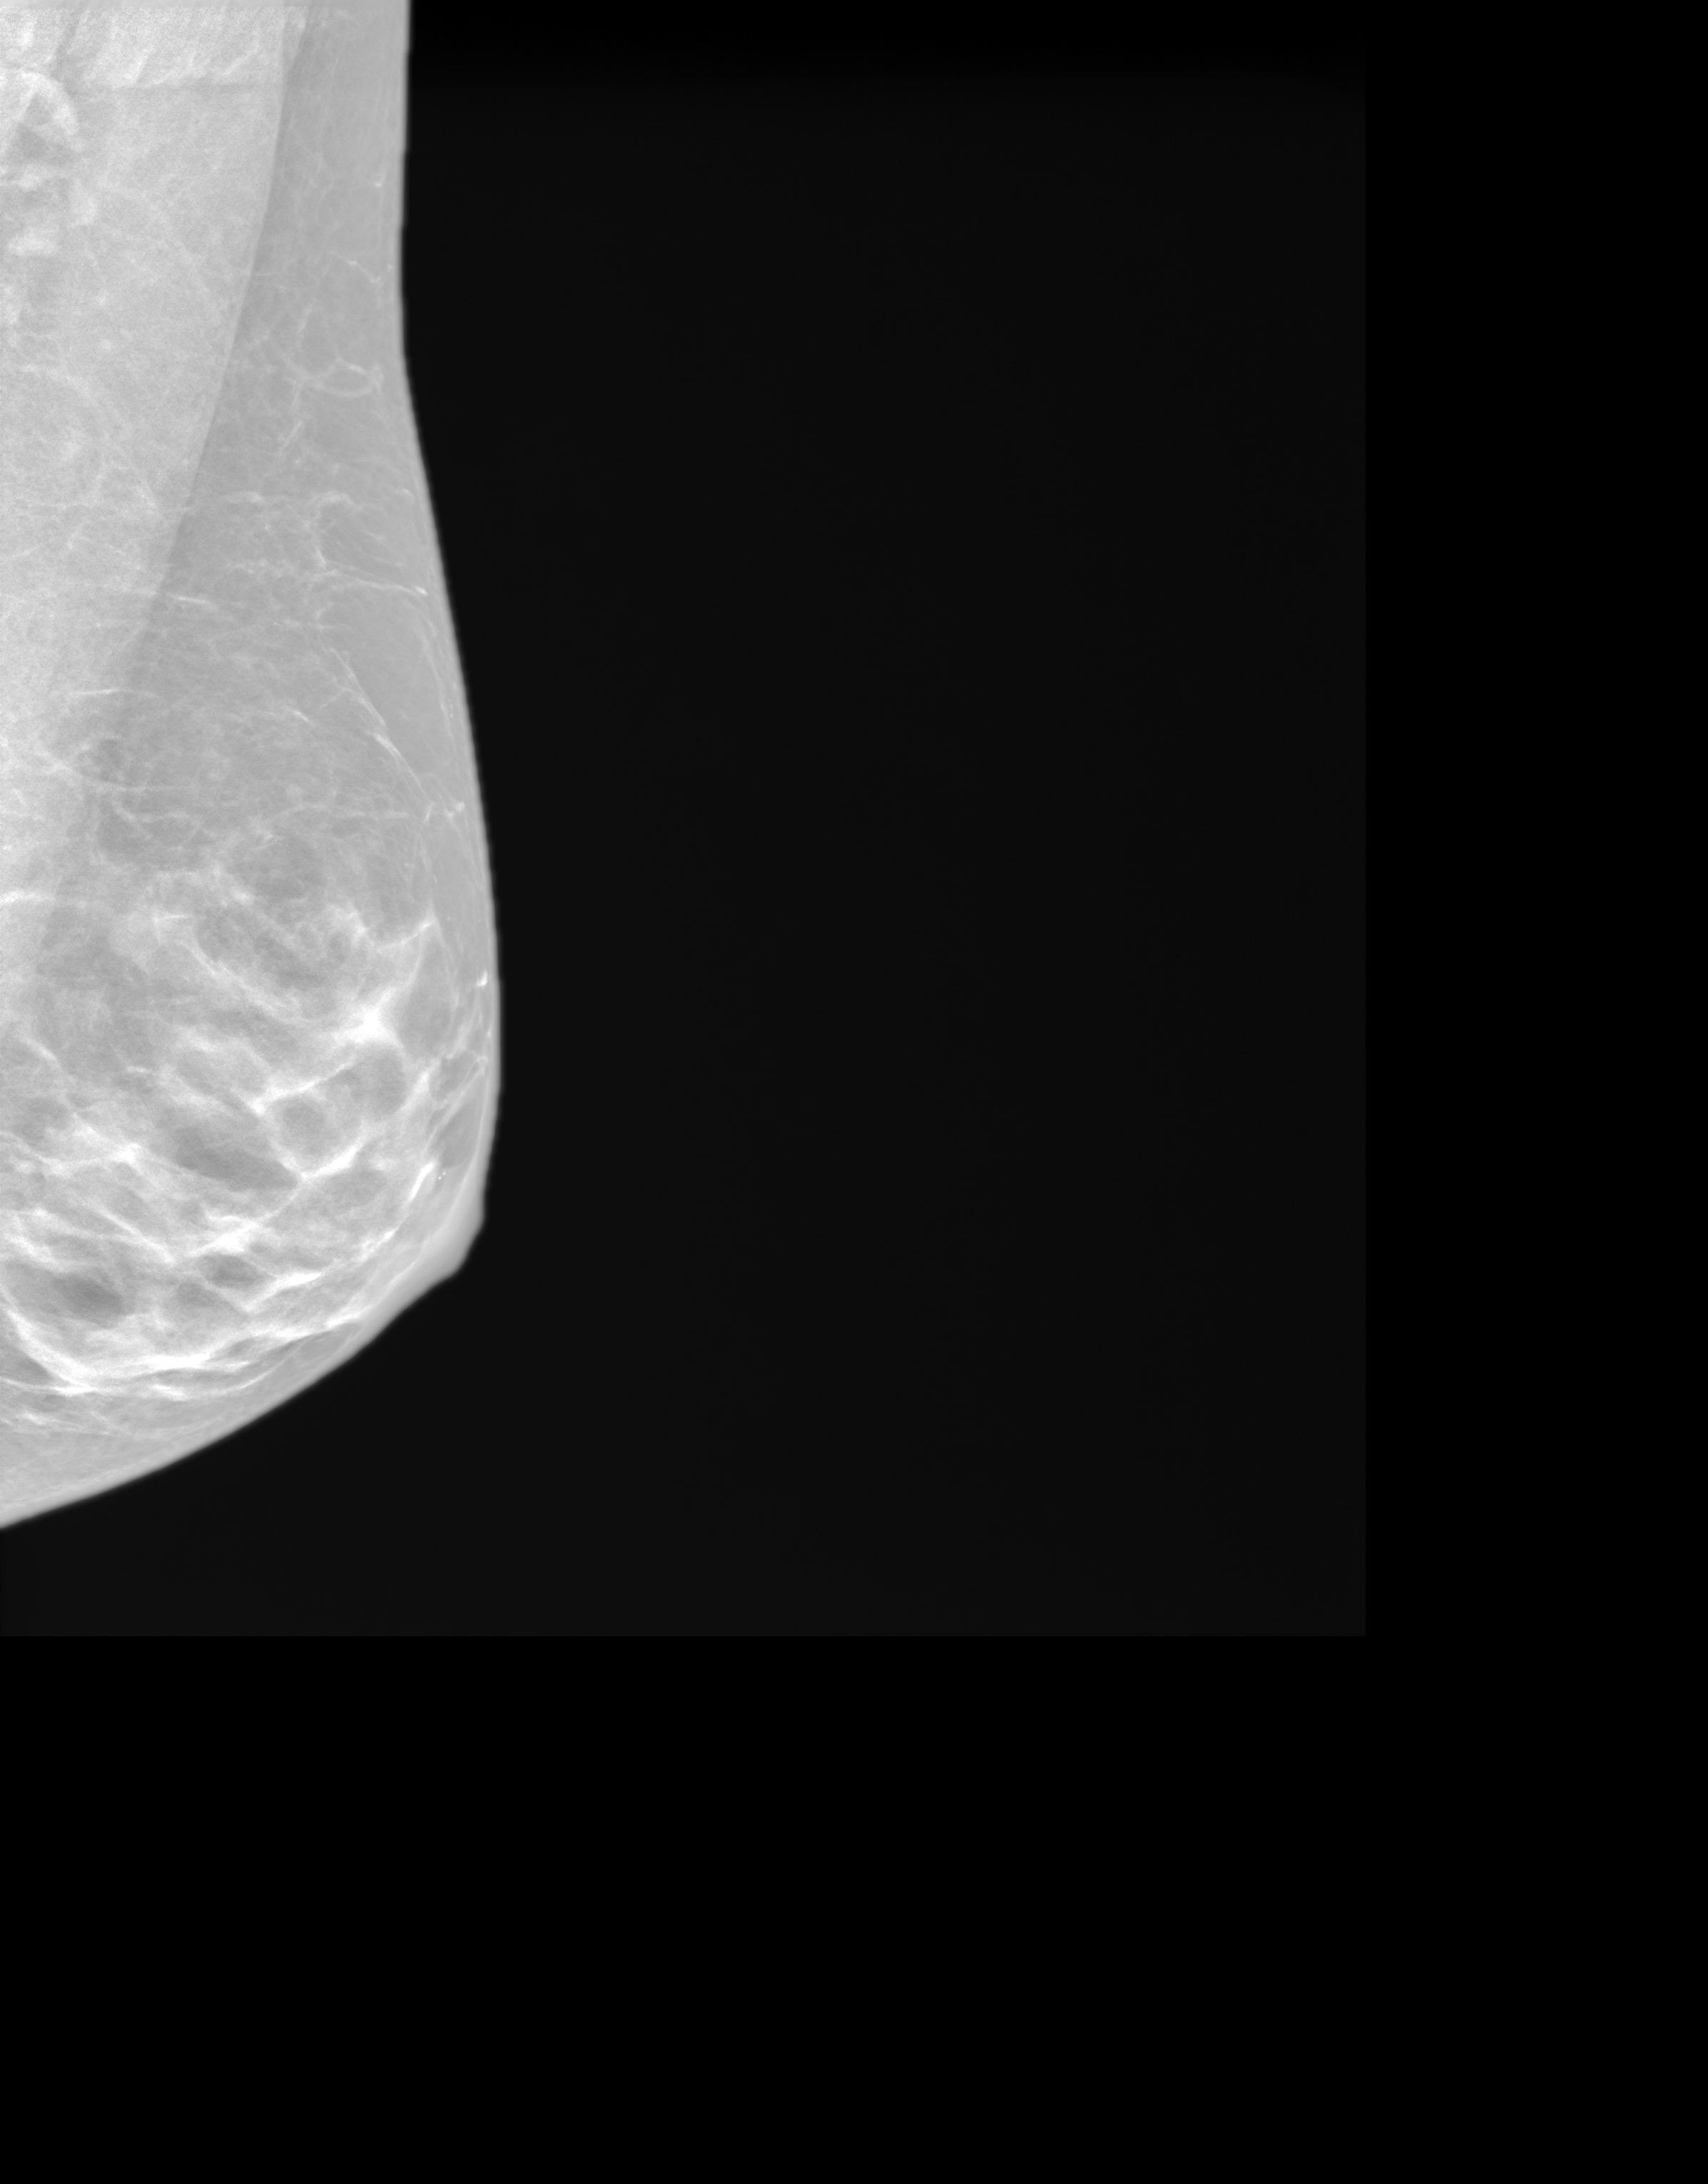
Synthesized 2-D mammogram reconstructed from digital breast tomosynthesis; left breast; mediolateral oblique (MLO) view; annual screening mammography examination. Patient aged 66 years (female).
- breast density at the screening exam (both breasts): heterogeneously dense (BI-RADS density category c)
- final BI-RADS category for the screening round (tomosynthesis exam, both breasts): category 1
- recall: no recall after this screen